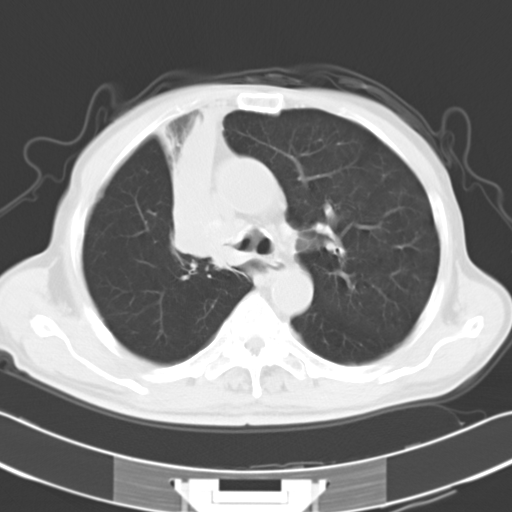
Chest CT, one axial slice; position 22 of 31 along the scan axis; lung window (W 1500 / L -600 HU); 10 mm slice thickness; 512 × 512 image matrix. Patient: male, 73 years. Case-level facts recorded for this patient, not image findings: clinical TNM (as recorded): T2a N1 M0.
Structures marked on this image (rectangle marked by the reading radiologist):
- lung tumour (recorded histology: squamous cell carcinoma): bounding box [x1, y1, x2, y2] px = [152, 102, 225, 274]